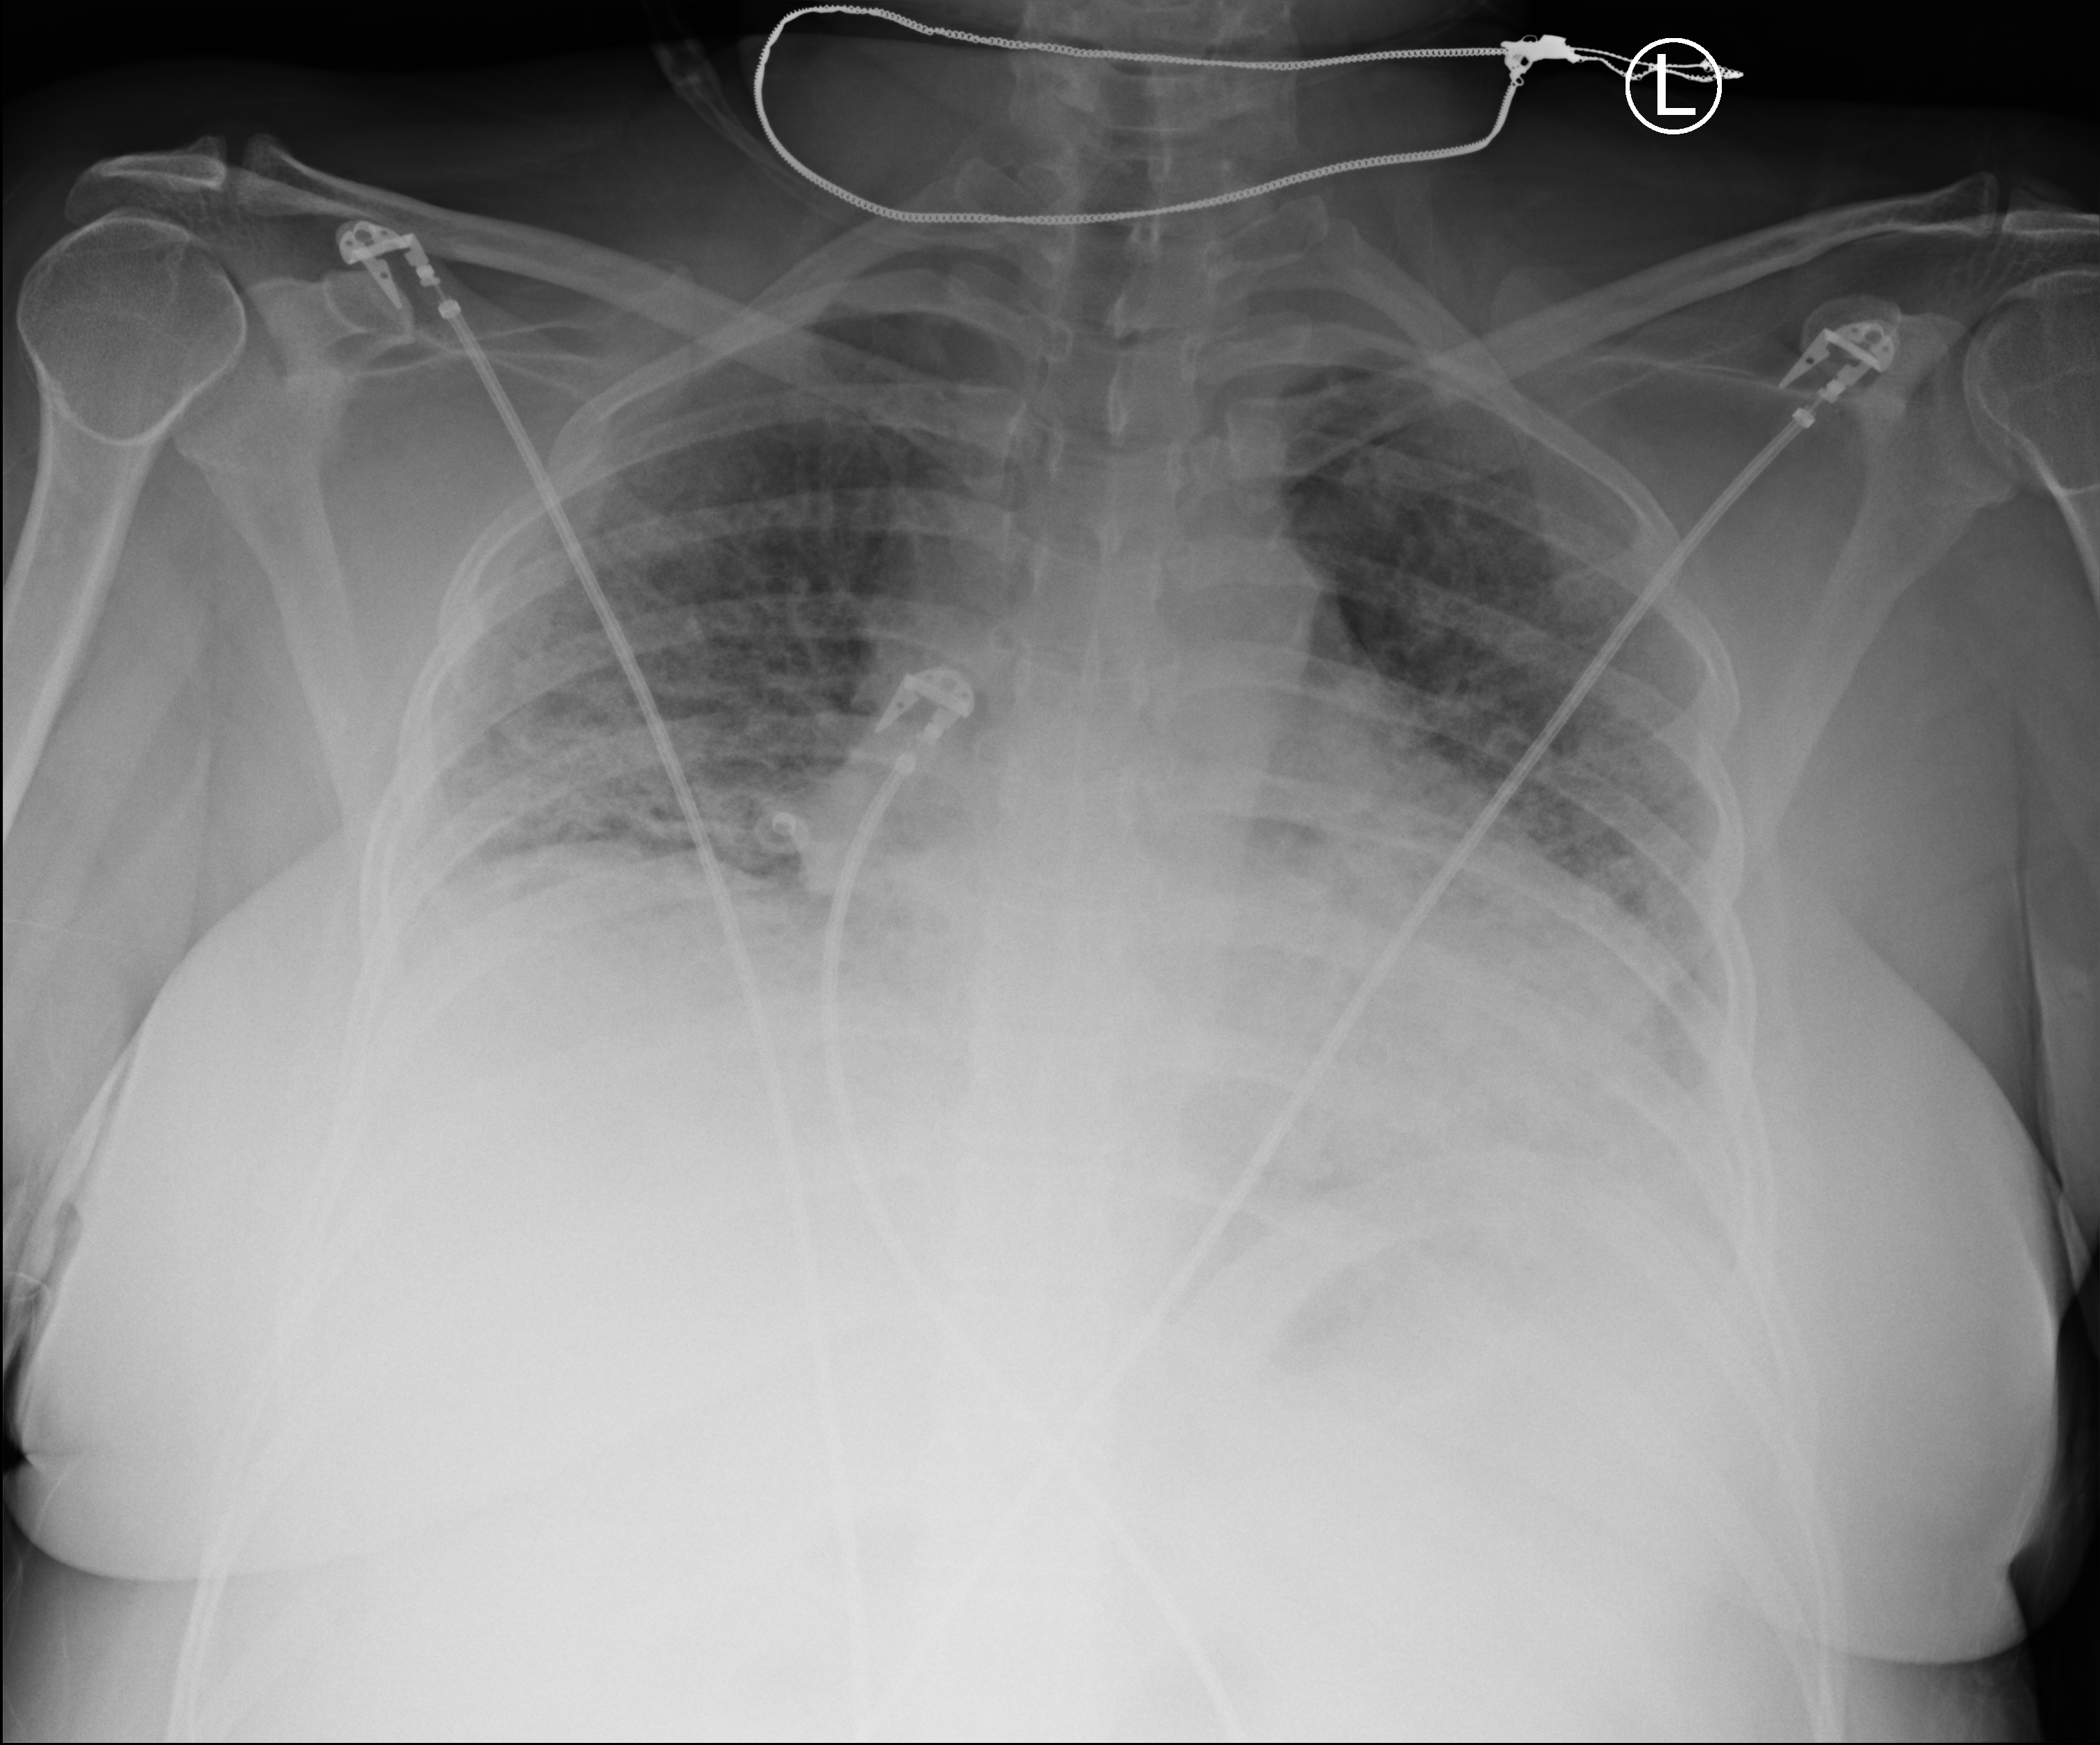
Bedside chest radiograph (computed radiography), anteroposterior (AP) projection. Female patient hospitalised with COVID-19, age 18–59 years.
Admission-level facts for this patient (not findings on this image; timing relative to this image not recorded): diabetes (admission record): no; admitted to intensive care during this hospital stay: yes.